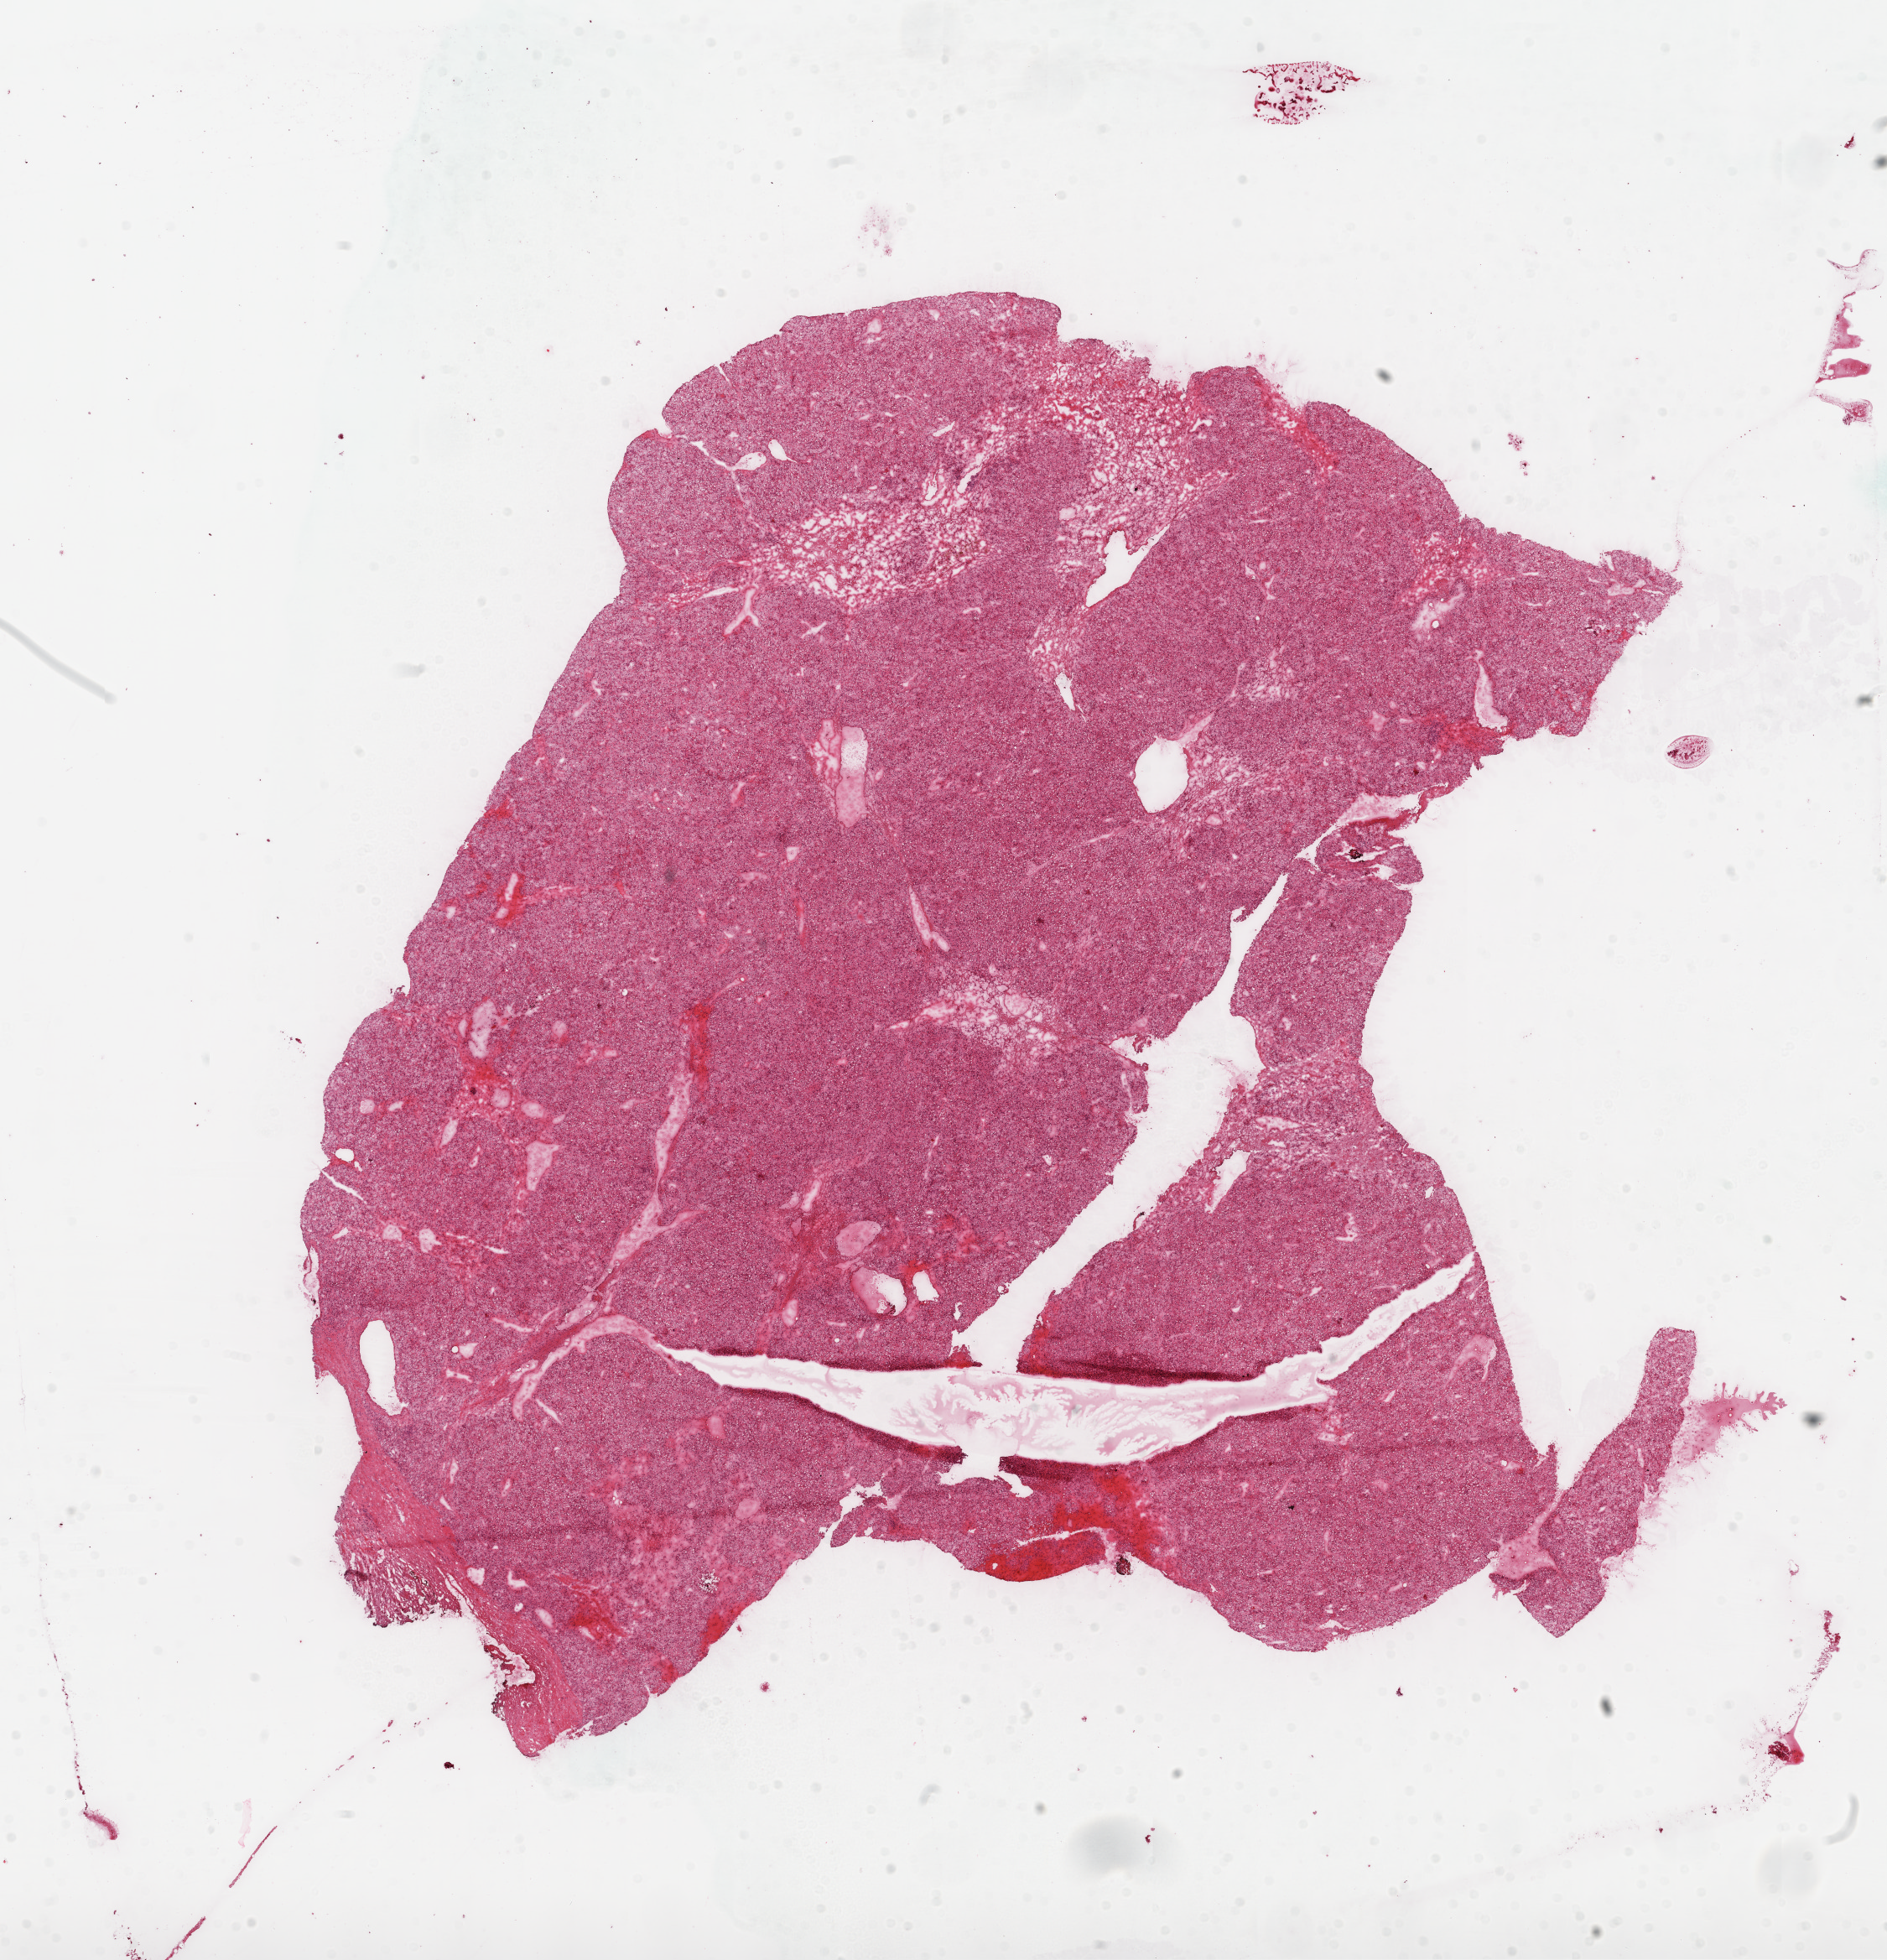
Whole-slide histology image, H&E-stained, low-resolution overview of the scanned area, about 18.1 x 18.8 mm (from a 20x scan); frozen section; kidney, primary tumour sample. Male, age 74 years at initial diagnosis. Histologic grade: G2 (moderately differentiated). Slide review estimates, as recorded: tumour cells 95%, tumour nuclei 85%, normal cells 0%, stromal cells 5%, necrosis 0%.
Diagnosis: Clear cell adenocarcinoma, NOS. AJCC pathologic stage: III. TNM: T3b NX M0.